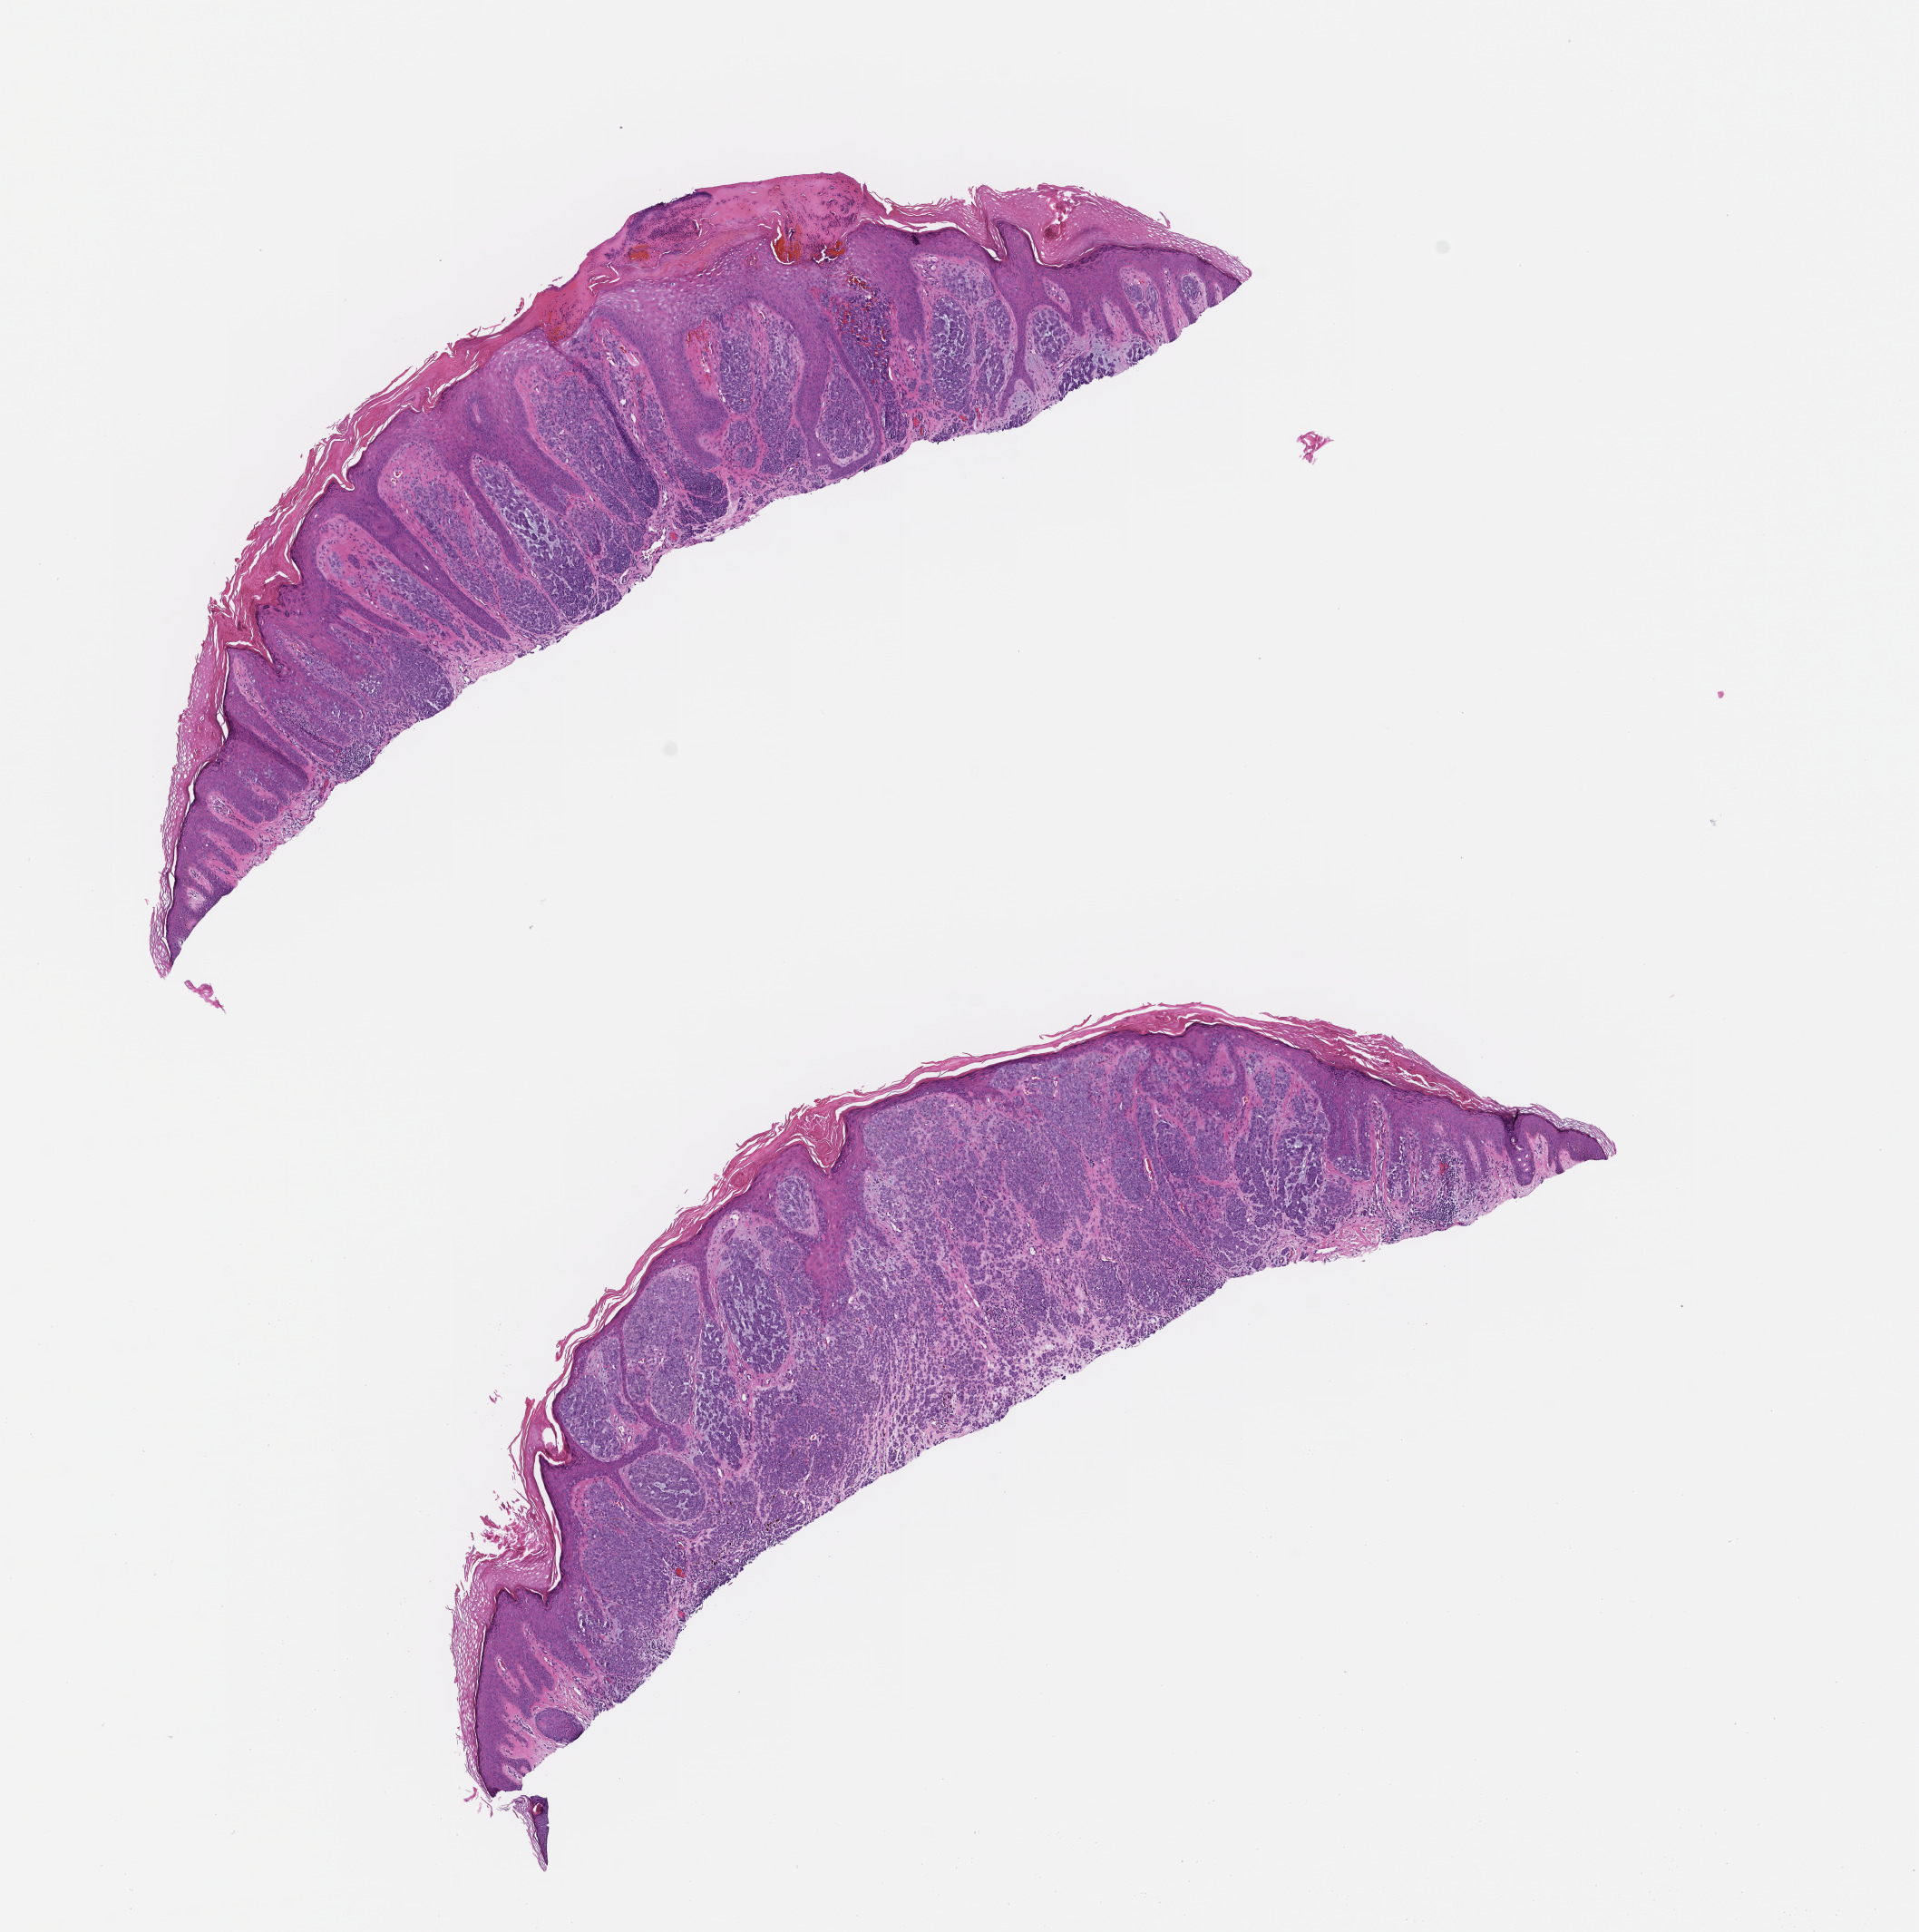
Hematoxylin and eosin (H&E) whole-slide image, whole scanned area (about 8.5 x 8.6 mm) shown as a low-resolution overview; formalin-fixed, paraffin-embedded (FFPE) tissue; site: skin; archival tissue. Patient: male.
This section: primary tumour tissue. Diagnosis: Melanoma.